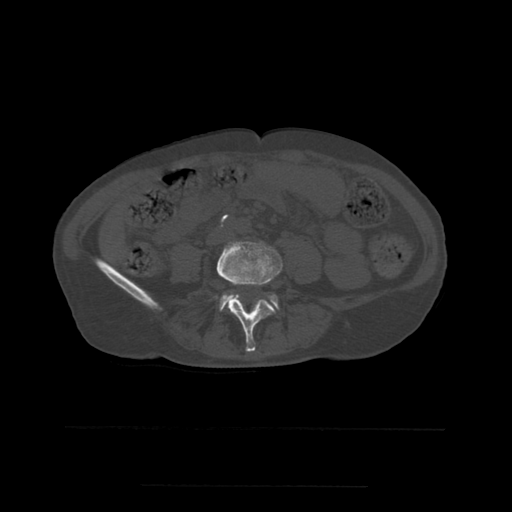
CT including the spine, one axial slice. Position 161 of 544 along the scan axis. Bone window (W 1800 / L 400 HU). 1.25 mm slice thickness. 512 × 512 image matrix, field of view 350 × 350 mm. Patient age 58 years. Case-level facts recorded for this patient, not image findings: primary cancer: lung.
Structures marked on this image (semi-automatically segmented with operator editing):
- L4 vertebra: box from (x=215, y=242) to (x=283, y=352) px
- L5 vertebra: (x=220, y=294)–(x=279, y=311)